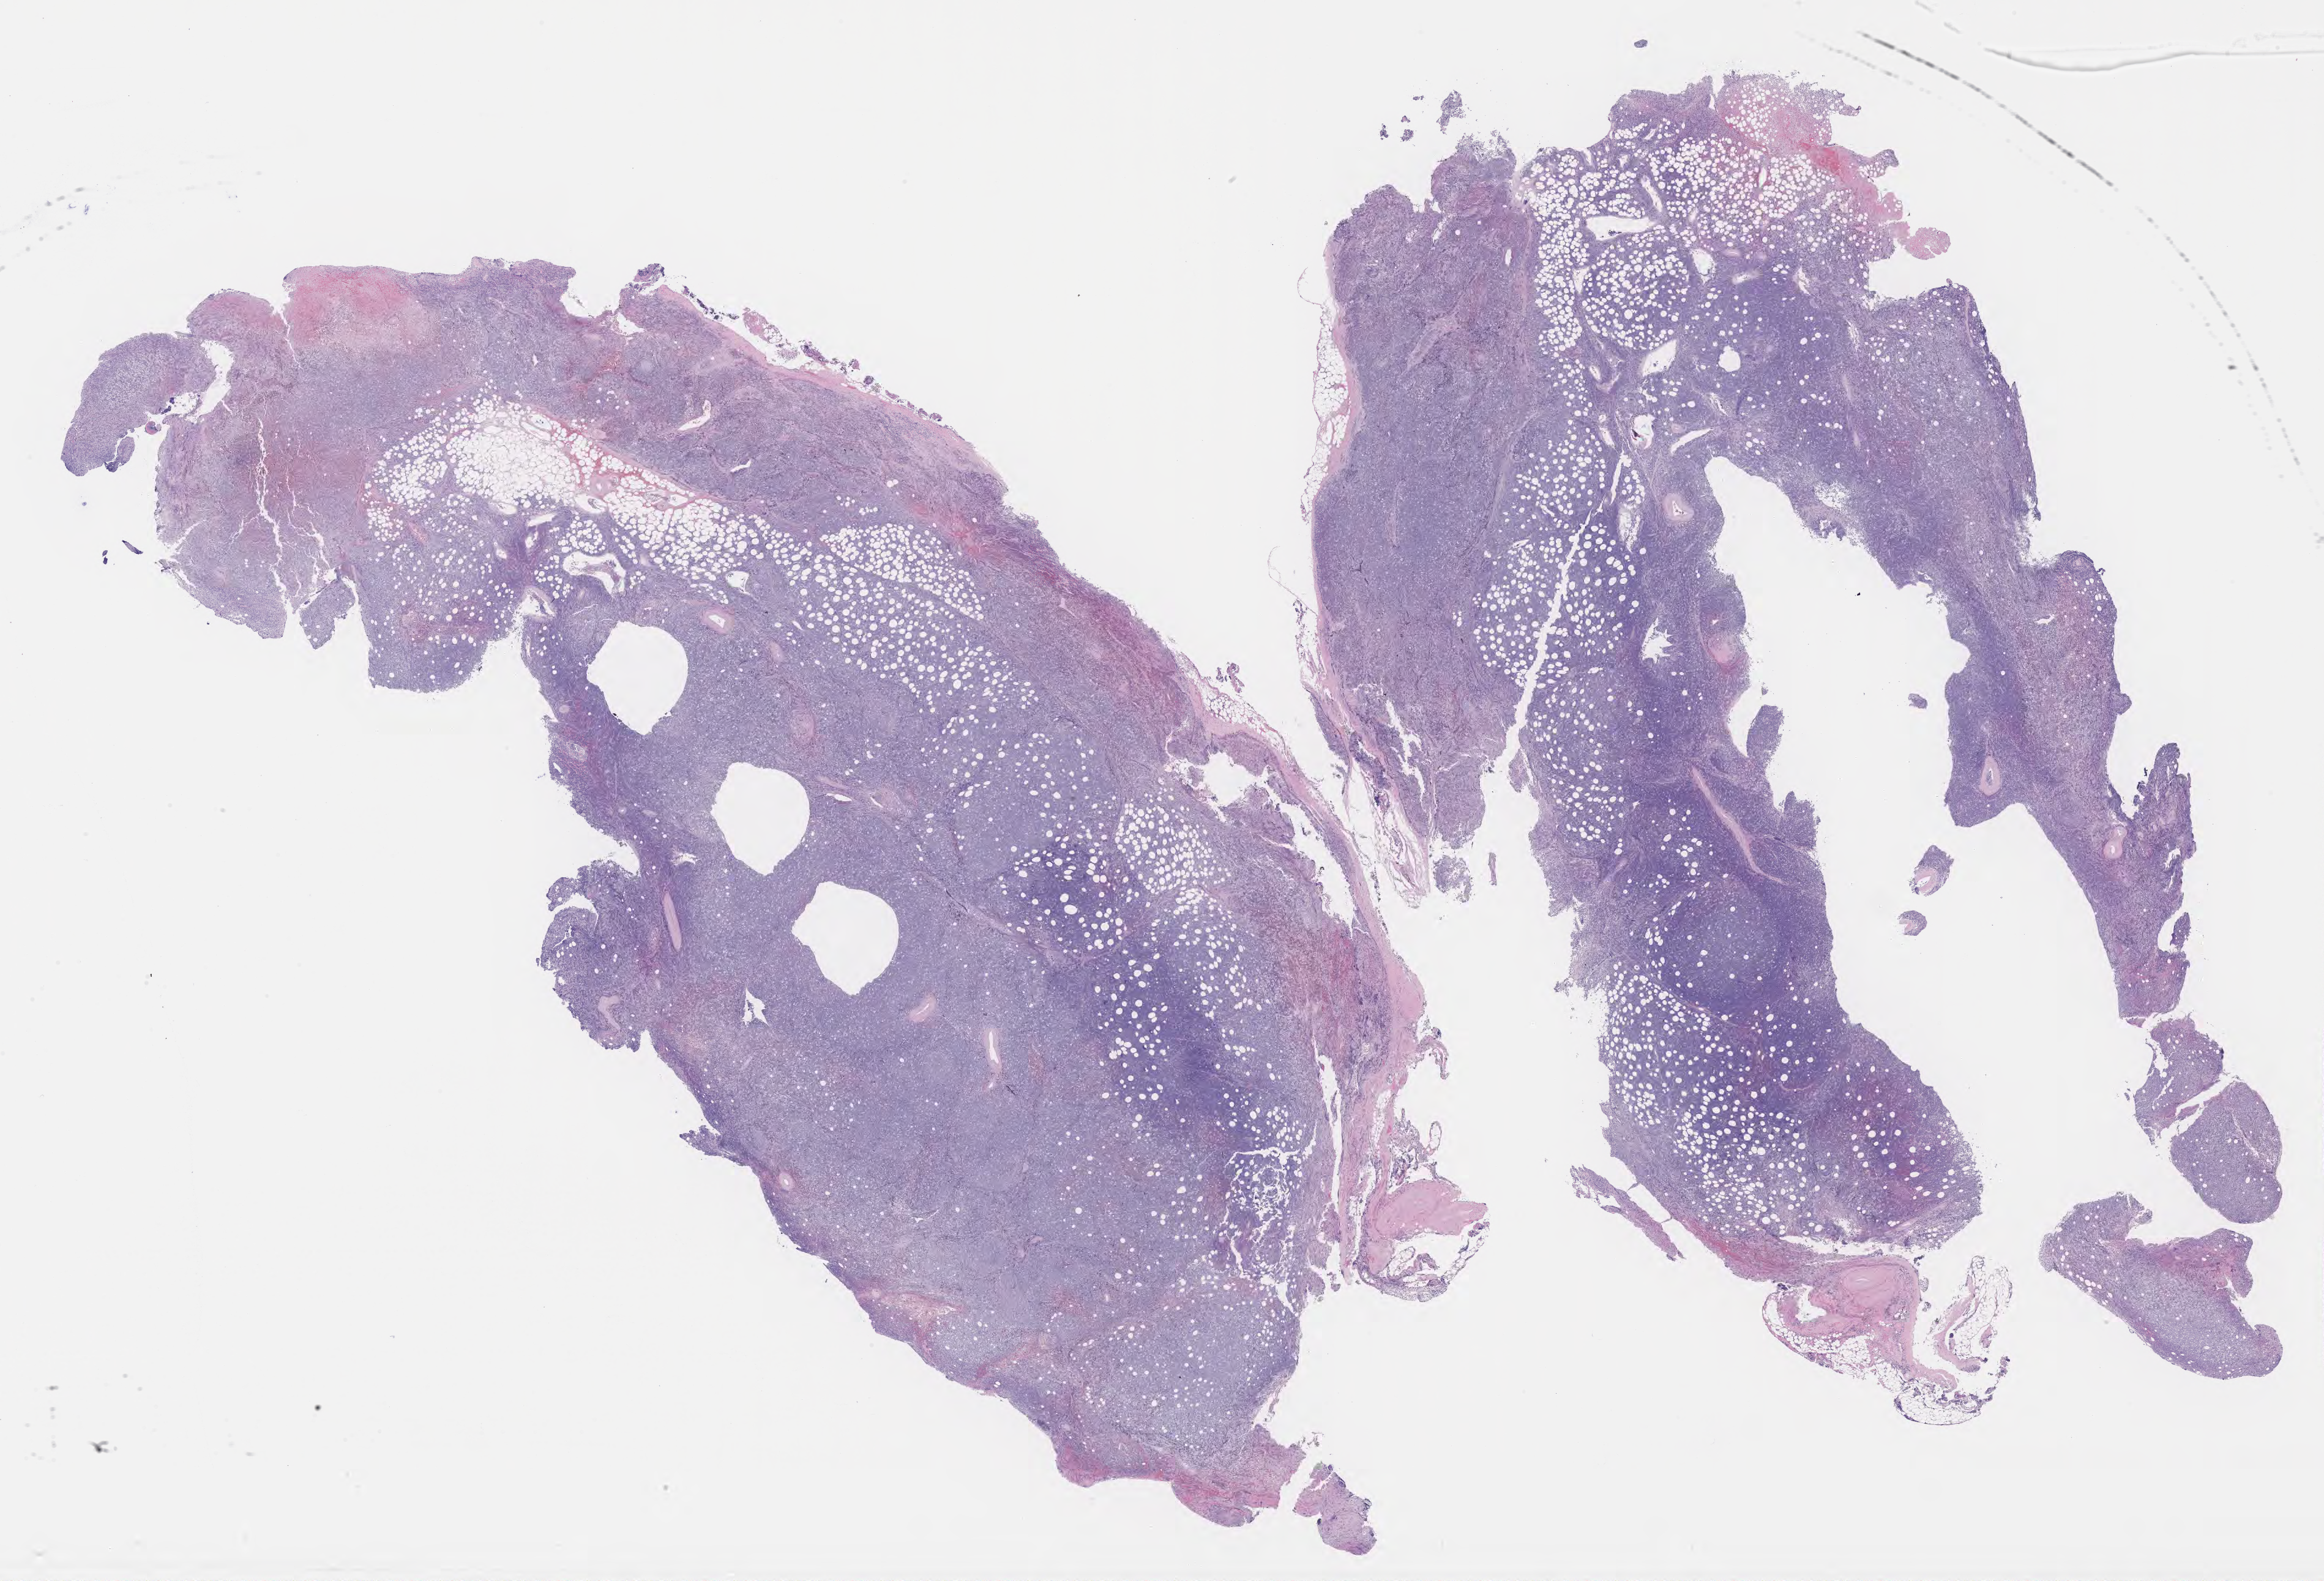
H&E whole-slide image, low-resolution overview of the scanned area, about 30.7 x 20.9 mm, tumor tissue, site: lower limb lymph node. Patient: male, age 45 years.
- diagnosis: Burkitt lymphoma, NOS